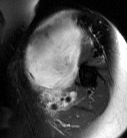
MRI of an extremity soft-tissue mass, one axial slice. Slice 52 of 87 in the series (ordered by position). T2-weighted fat-saturated. MR volume resampled by the dataset authors to the PET/CT grid (not the native acquisition matrix). 3.27 mm slice thickness. 127 × 138 image matrix, field of view 124 × 135 mm. Female patient. Case-level facts recorded for this patient, not image findings: histological type: pleiomorphic leiomyosarcoma; grade: high; site of the primary tumour: left biceps.
Annotated regions visible in this slice (expert contour drawn on MRI and transferred to this co-registered scan by the dataset authors):
- gross tumour volume including surrounding oedema: bounding box [x1, y1, x2, y2] px = [24, 20, 87, 108]
- gross tumour volume (mass): [24, 21, 83, 94]